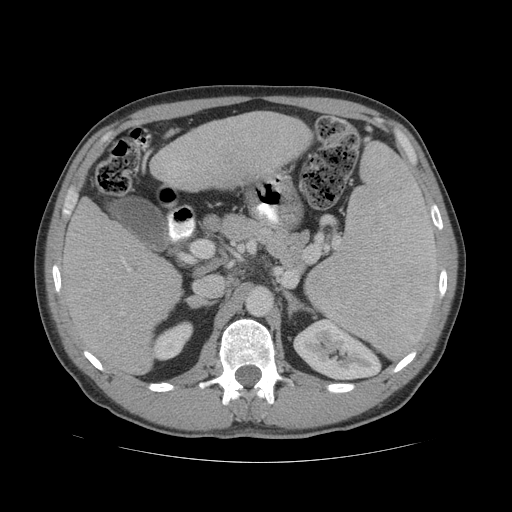
Contrast-enhanced abdominal CT (liver protocol), one axial slice; position 31 of 81 along the scan axis; 140 kVp; soft-tissue window (W 400 / L 40 HU); 2.5 mm slice thickness; 512 × 512 image matrix, field of view 400 × 400 mm. From the clinical record (not read from this slice): diagnosis: hepatocellular carcinoma (patient treated with transarterial chemoembolisation; whether this scan precedes or follows treatment is not stated here); TNM stage (as recorded): Stage-IVB; Child-Pugh class: B; tumour differentiation: well differentiated; tumour nodularity: multinodular.
Structures marked on this image (semi-automatic segmentation, software-assisted and operator-edited):
- liver parenchyma outside the tumour (the mass and vessels are separate outlines, so this box may not span the whole liver): box from (x=60, y=112) to (x=312, y=374) px
- liver vessels: (x=123, y=161)–(x=188, y=271)